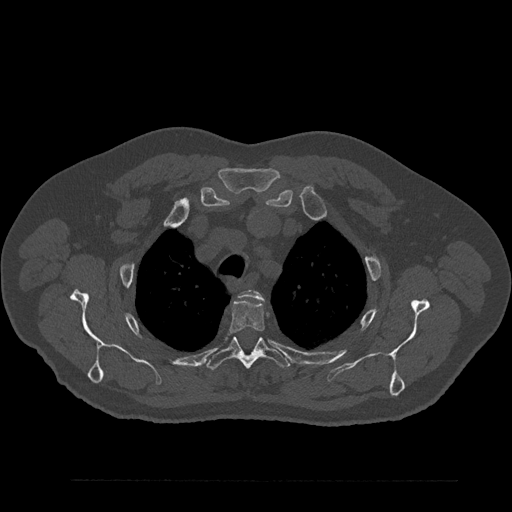
CT including the spine, one axial slice; position 667 of 797 along the scan axis; reconstruction kernel Br40s/3; bone window (W 1800 / L 400 HU); 0.5 mm slice thickness; 512 × 512 image matrix, field of view 430 × 430 mm. Male patient, age 61 years. Case-level facts recorded for this patient, not image findings: primary cancer: prostate.
Annotated regions visible in this slice (semi-automatically segmented with operator editing):
- T2 vertebra: bounding box <240,290,263,300> (left, top, right, bottom; pixels)
- T3 vertebra: <228,299,265,334>
- T4 vertebra: <207,336,290,370>